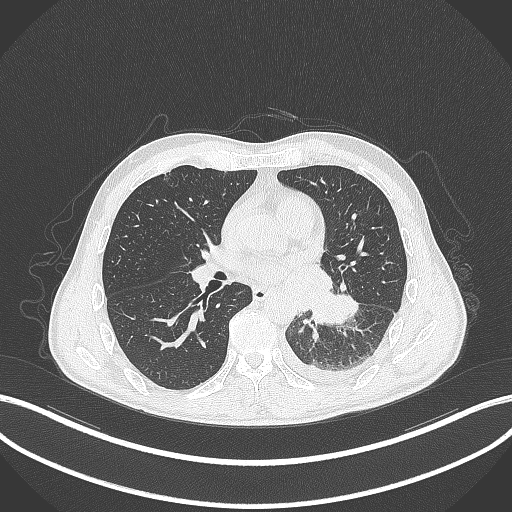
Chest CT, one axial slice; position 157 of 295 along the scan axis; 120 kVp; lung window (W 1500 / L -600 HU); 512 × 512 image matrix. Patient: male, 47 years. From the clinical record (not read from this slice): clinical TNM (as recorded): T3 N1 M1c.
Annotated regions visible in this slice (rectangle marked by the reading radiologist):
- lung tumour (recorded histology: small cell carcinoma): bounding box [x1, y1, x2, y2] px = [306, 287, 360, 331]